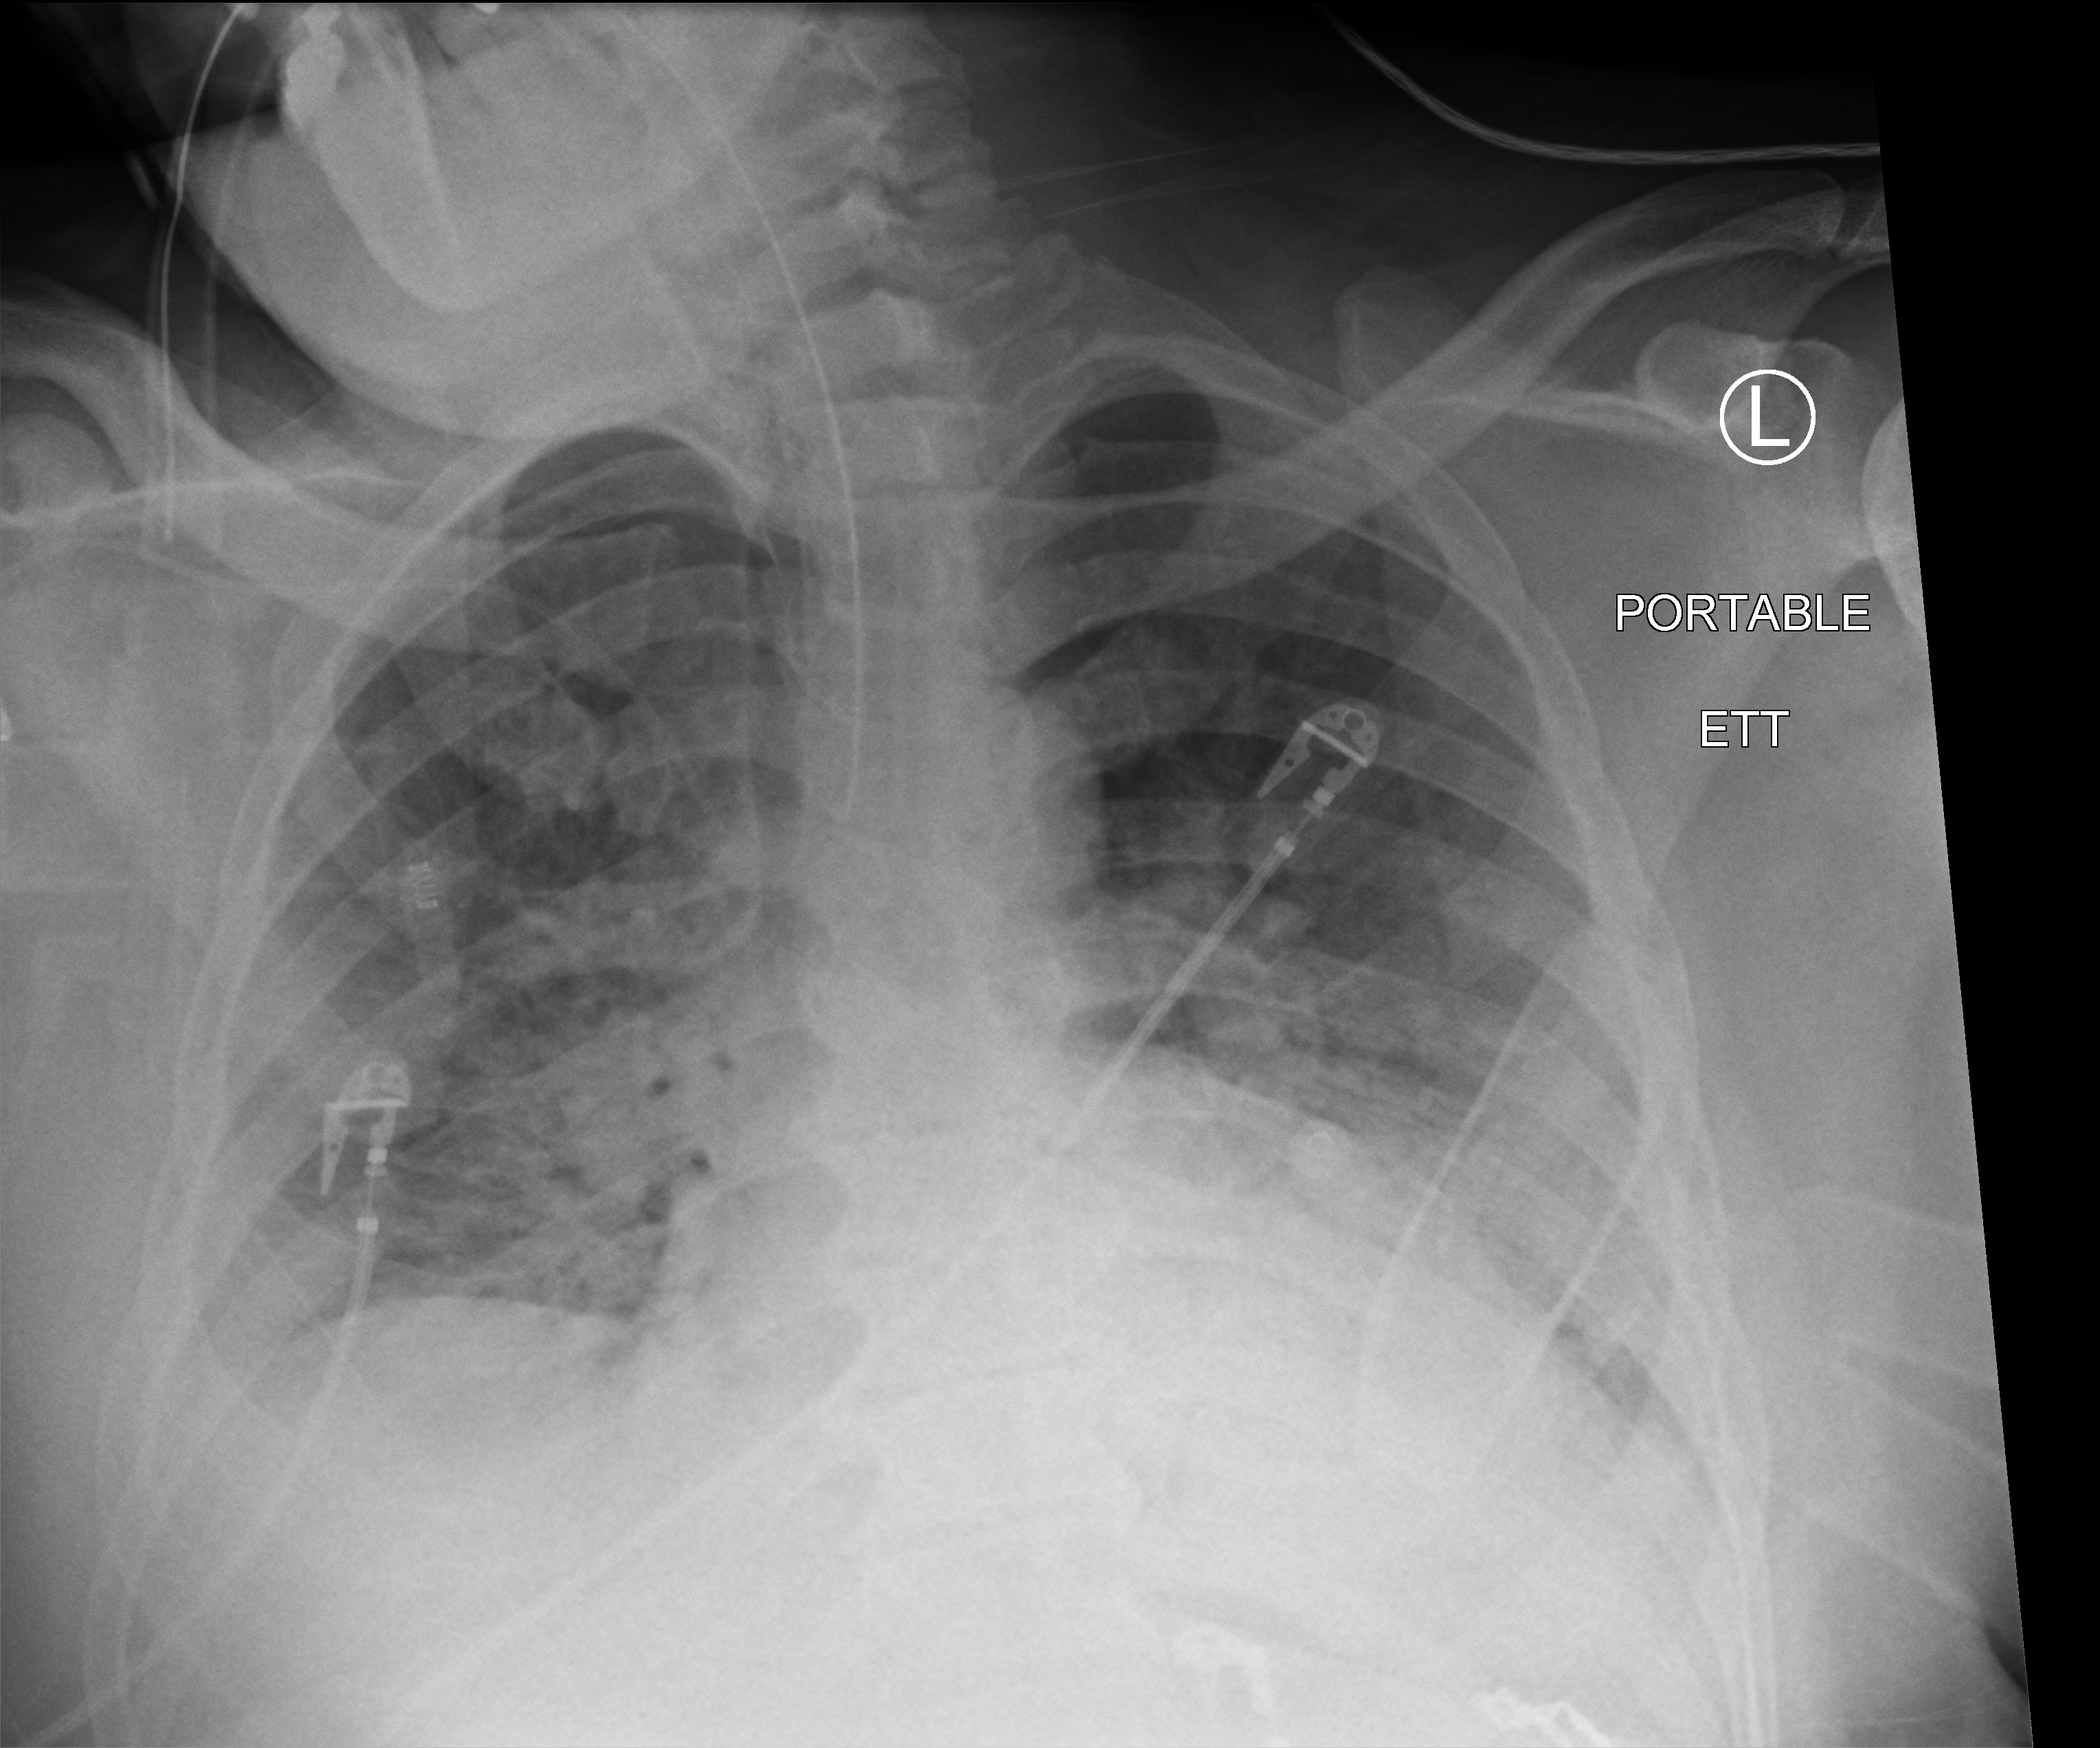
Portable chest radiograph; anteroposterior (AP) projection. Patient hospitalised with COVID-19; male, aged 18–59 years.
Admission-level facts for this patient (not findings on this image; timing relative to this image not recorded):
- admitted to intensive care during this hospital stay: yes
- chronic kidney disease (admission record): no
- mechanically ventilated during this hospital stay: yes